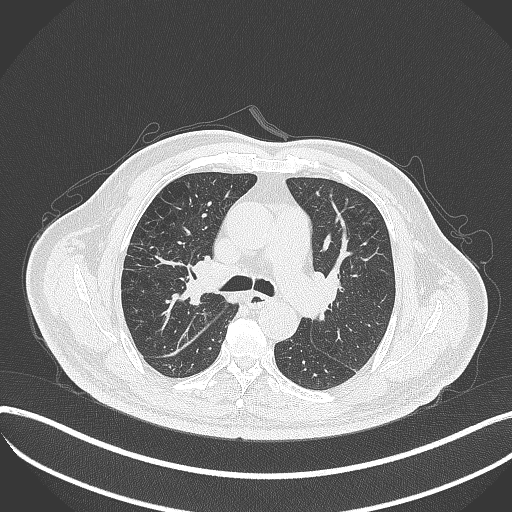
Chest CT, one axial slice. Slice 232 of 401 in the series (ordered by position). Reconstruction kernel B70f. Lung window (W 1500 / L -600 HU). 1 mm slice thickness. 512 × 512 image matrix, field of view 400 × 400 mm. Patient: male, 72 years. Case-level facts recorded for this patient, not image findings: clinical TNM (as recorded): T1c N0 M0.
Structures marked on this image (rectangle marked by the reading radiologist):
- lung tumour (recorded histology: squamous cell carcinoma): box from (x=177, y=259) to (x=207, y=308) px